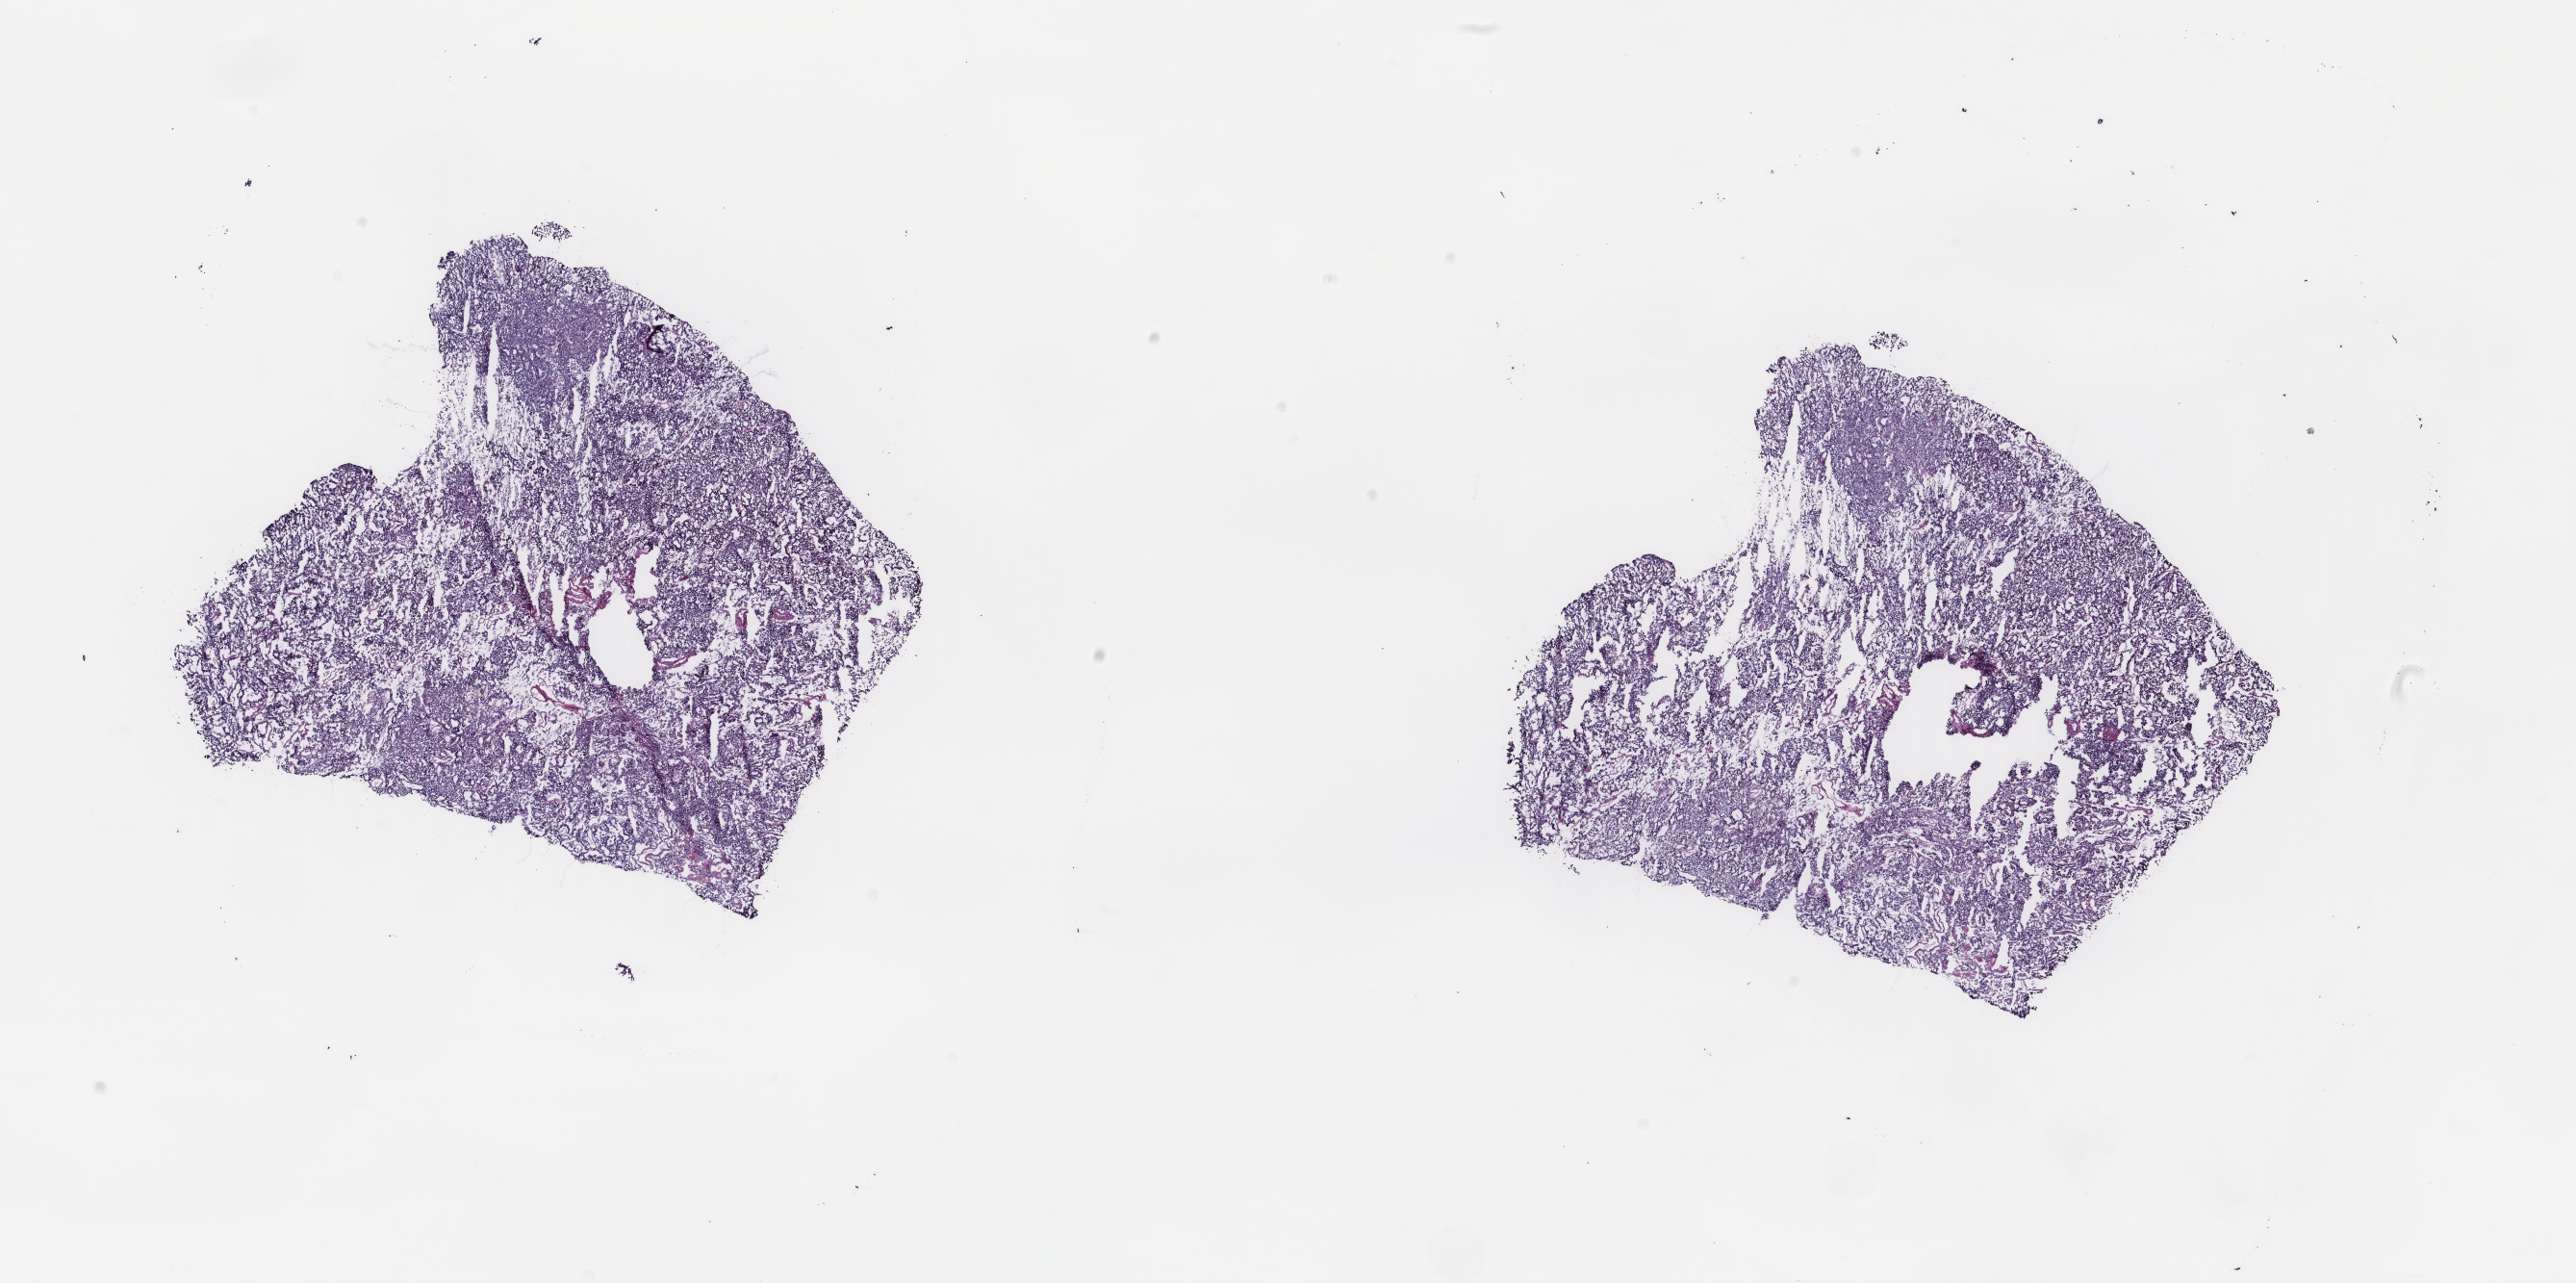
Hematoxylin and eosin (H&E) stained whole-slide image — low-resolution overview of the scanned area, about 21.2 x 10.6 mm (slide scanned at 40x); frozen section from the top of the tissue portion; primary tumour sample from the uterus. Female, age 76 years at initial diagnosis. Histologic grade: G2 (moderately differentiated). Pathologist review of this section (percent, as recorded): tumour cells 60%, tumour nuclei 60%, normal cells 0%, stromal cells 30%, necrosis 10%. Inflammatory infiltration, as recorded: lymphocyte infiltration 40%, monocyte infiltration 20%, neutrophil infiltration 20%.
Diagnosis: Endometrioid adenocarcinoma, NOS (endometrium). FIGO stage: IIIA.